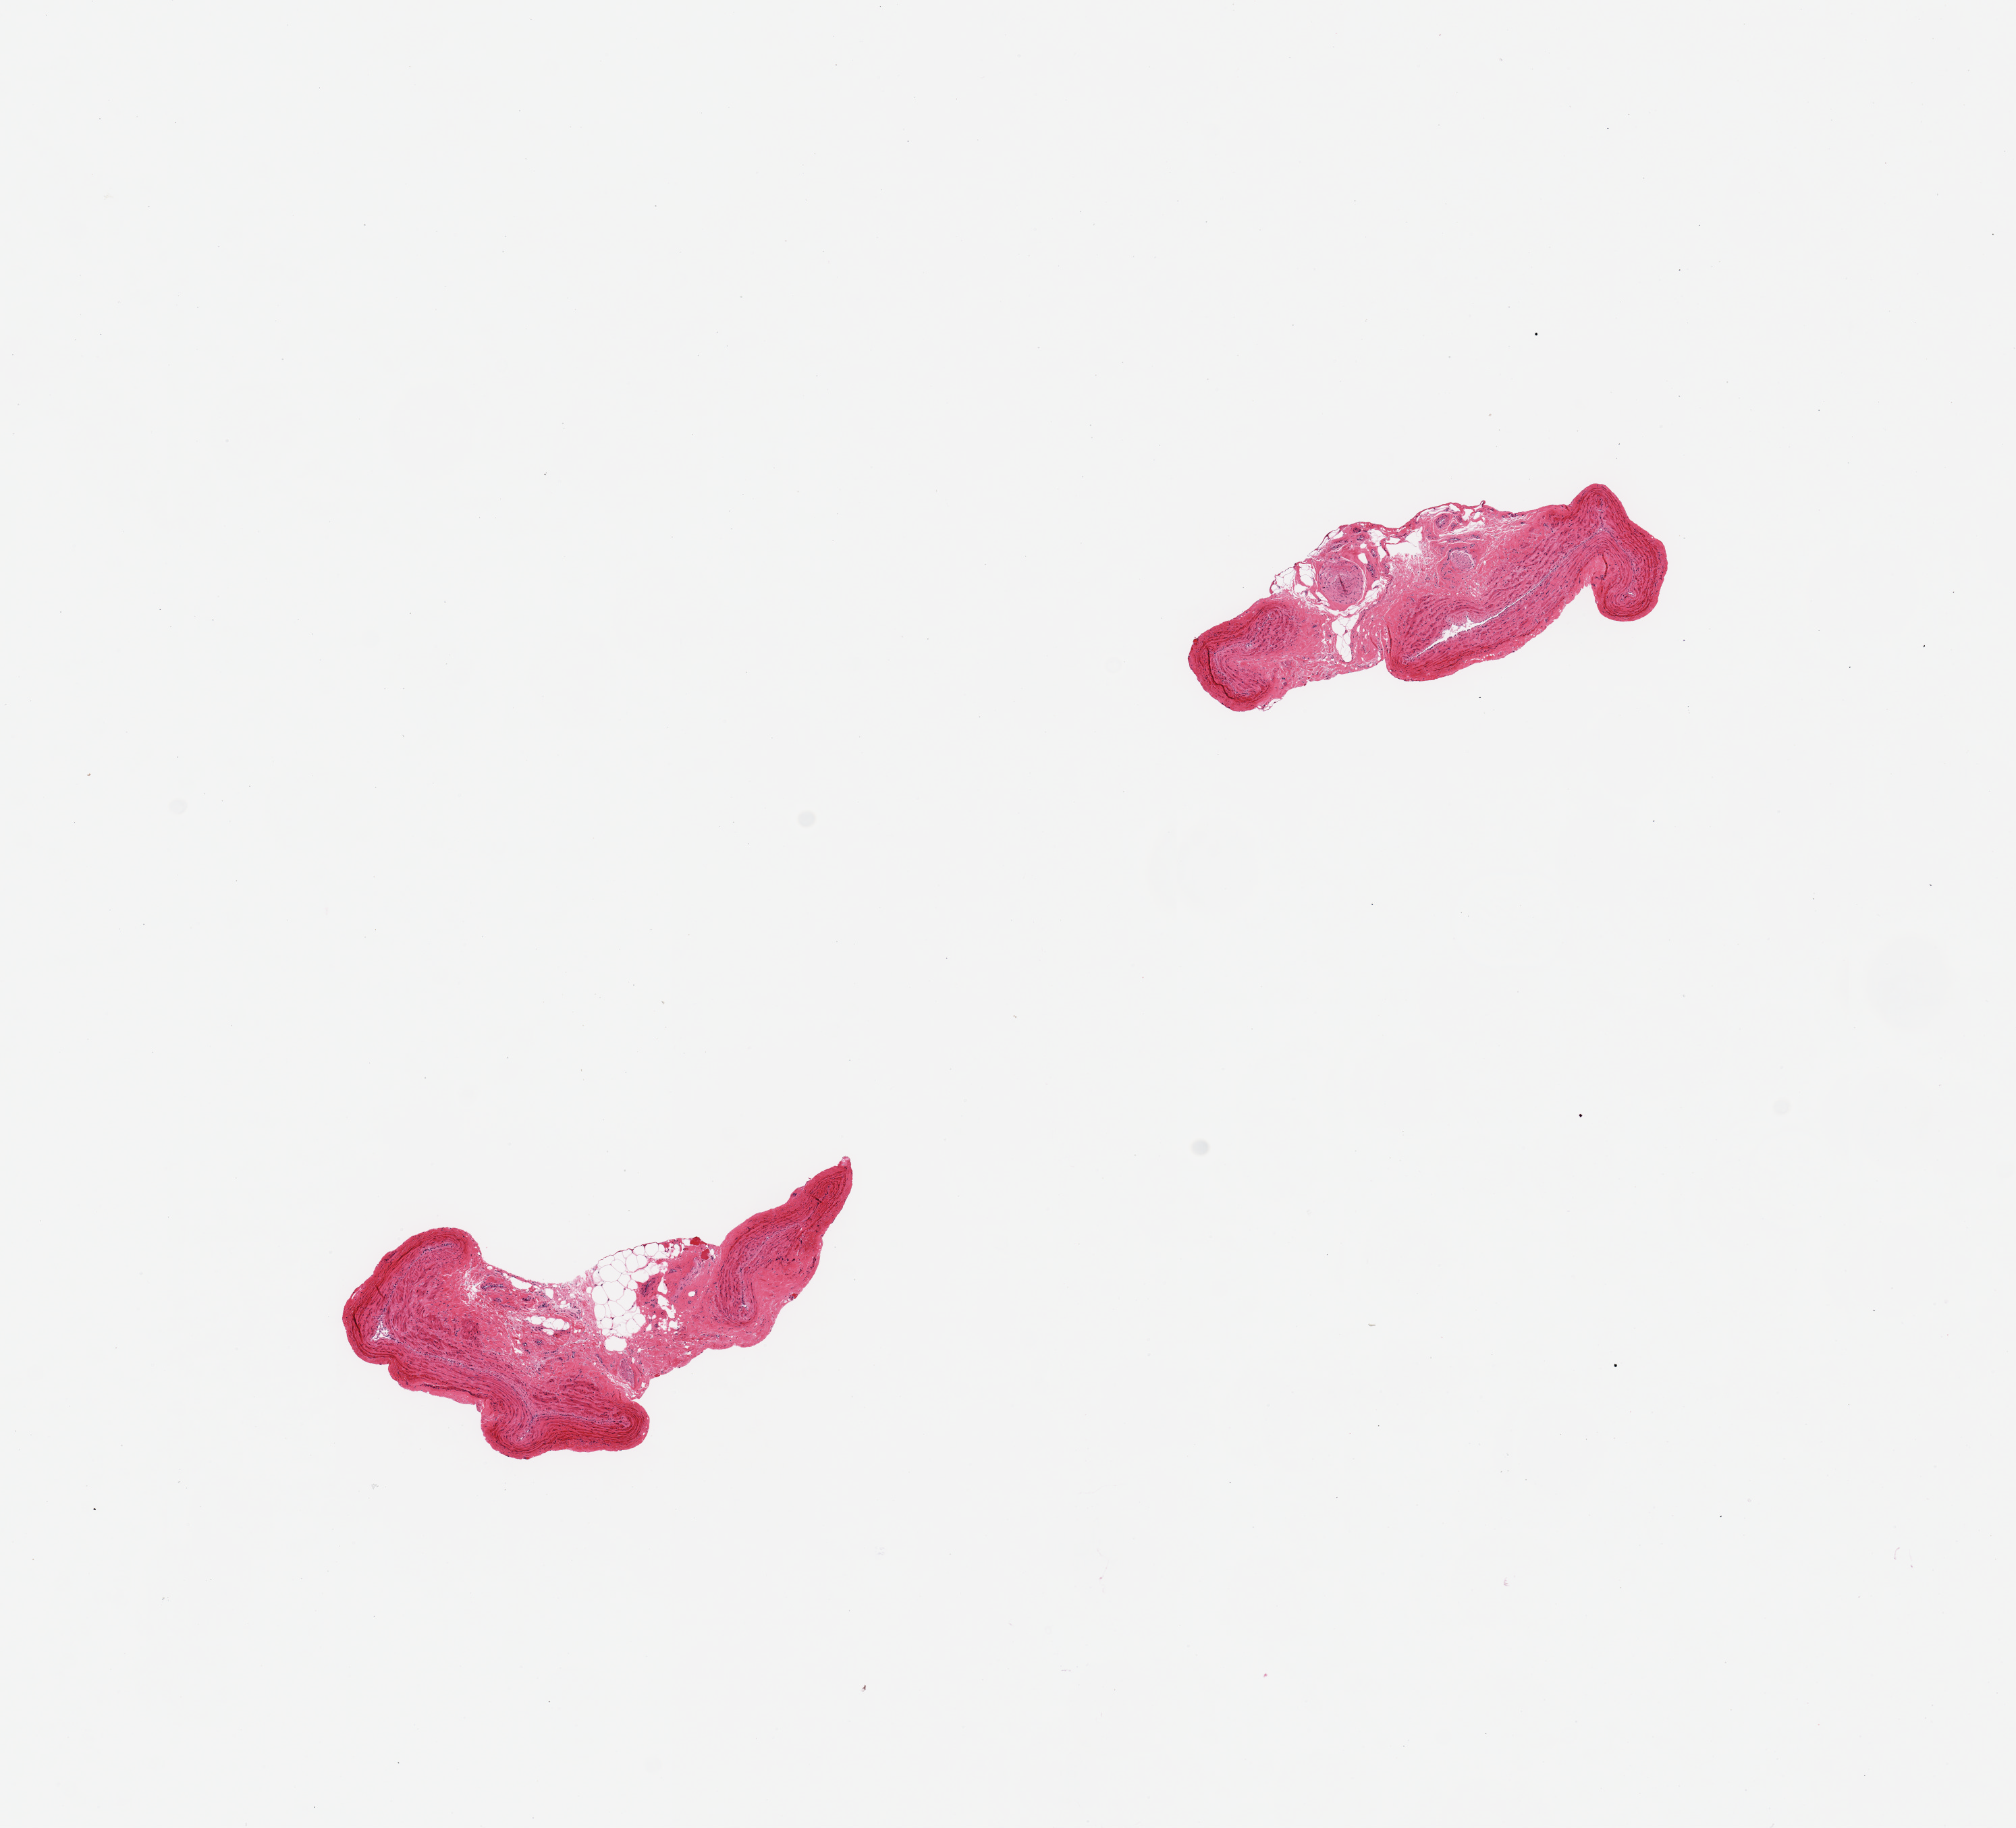
Digitized hematoxylin and eosin (H&E)-stained section, shown as a low-resolution overview of the whole scanned area (about 11.8 x 10.7 mm). PAXgene-fixed paraffin-embedded (PFPE) section. Target tissue: tibial artery. Tissue donor sample. Donor sex: male.
Review note (as recorded): 2 pieces; longitudinal sections with up to 30% fatty stroma; no plaque.